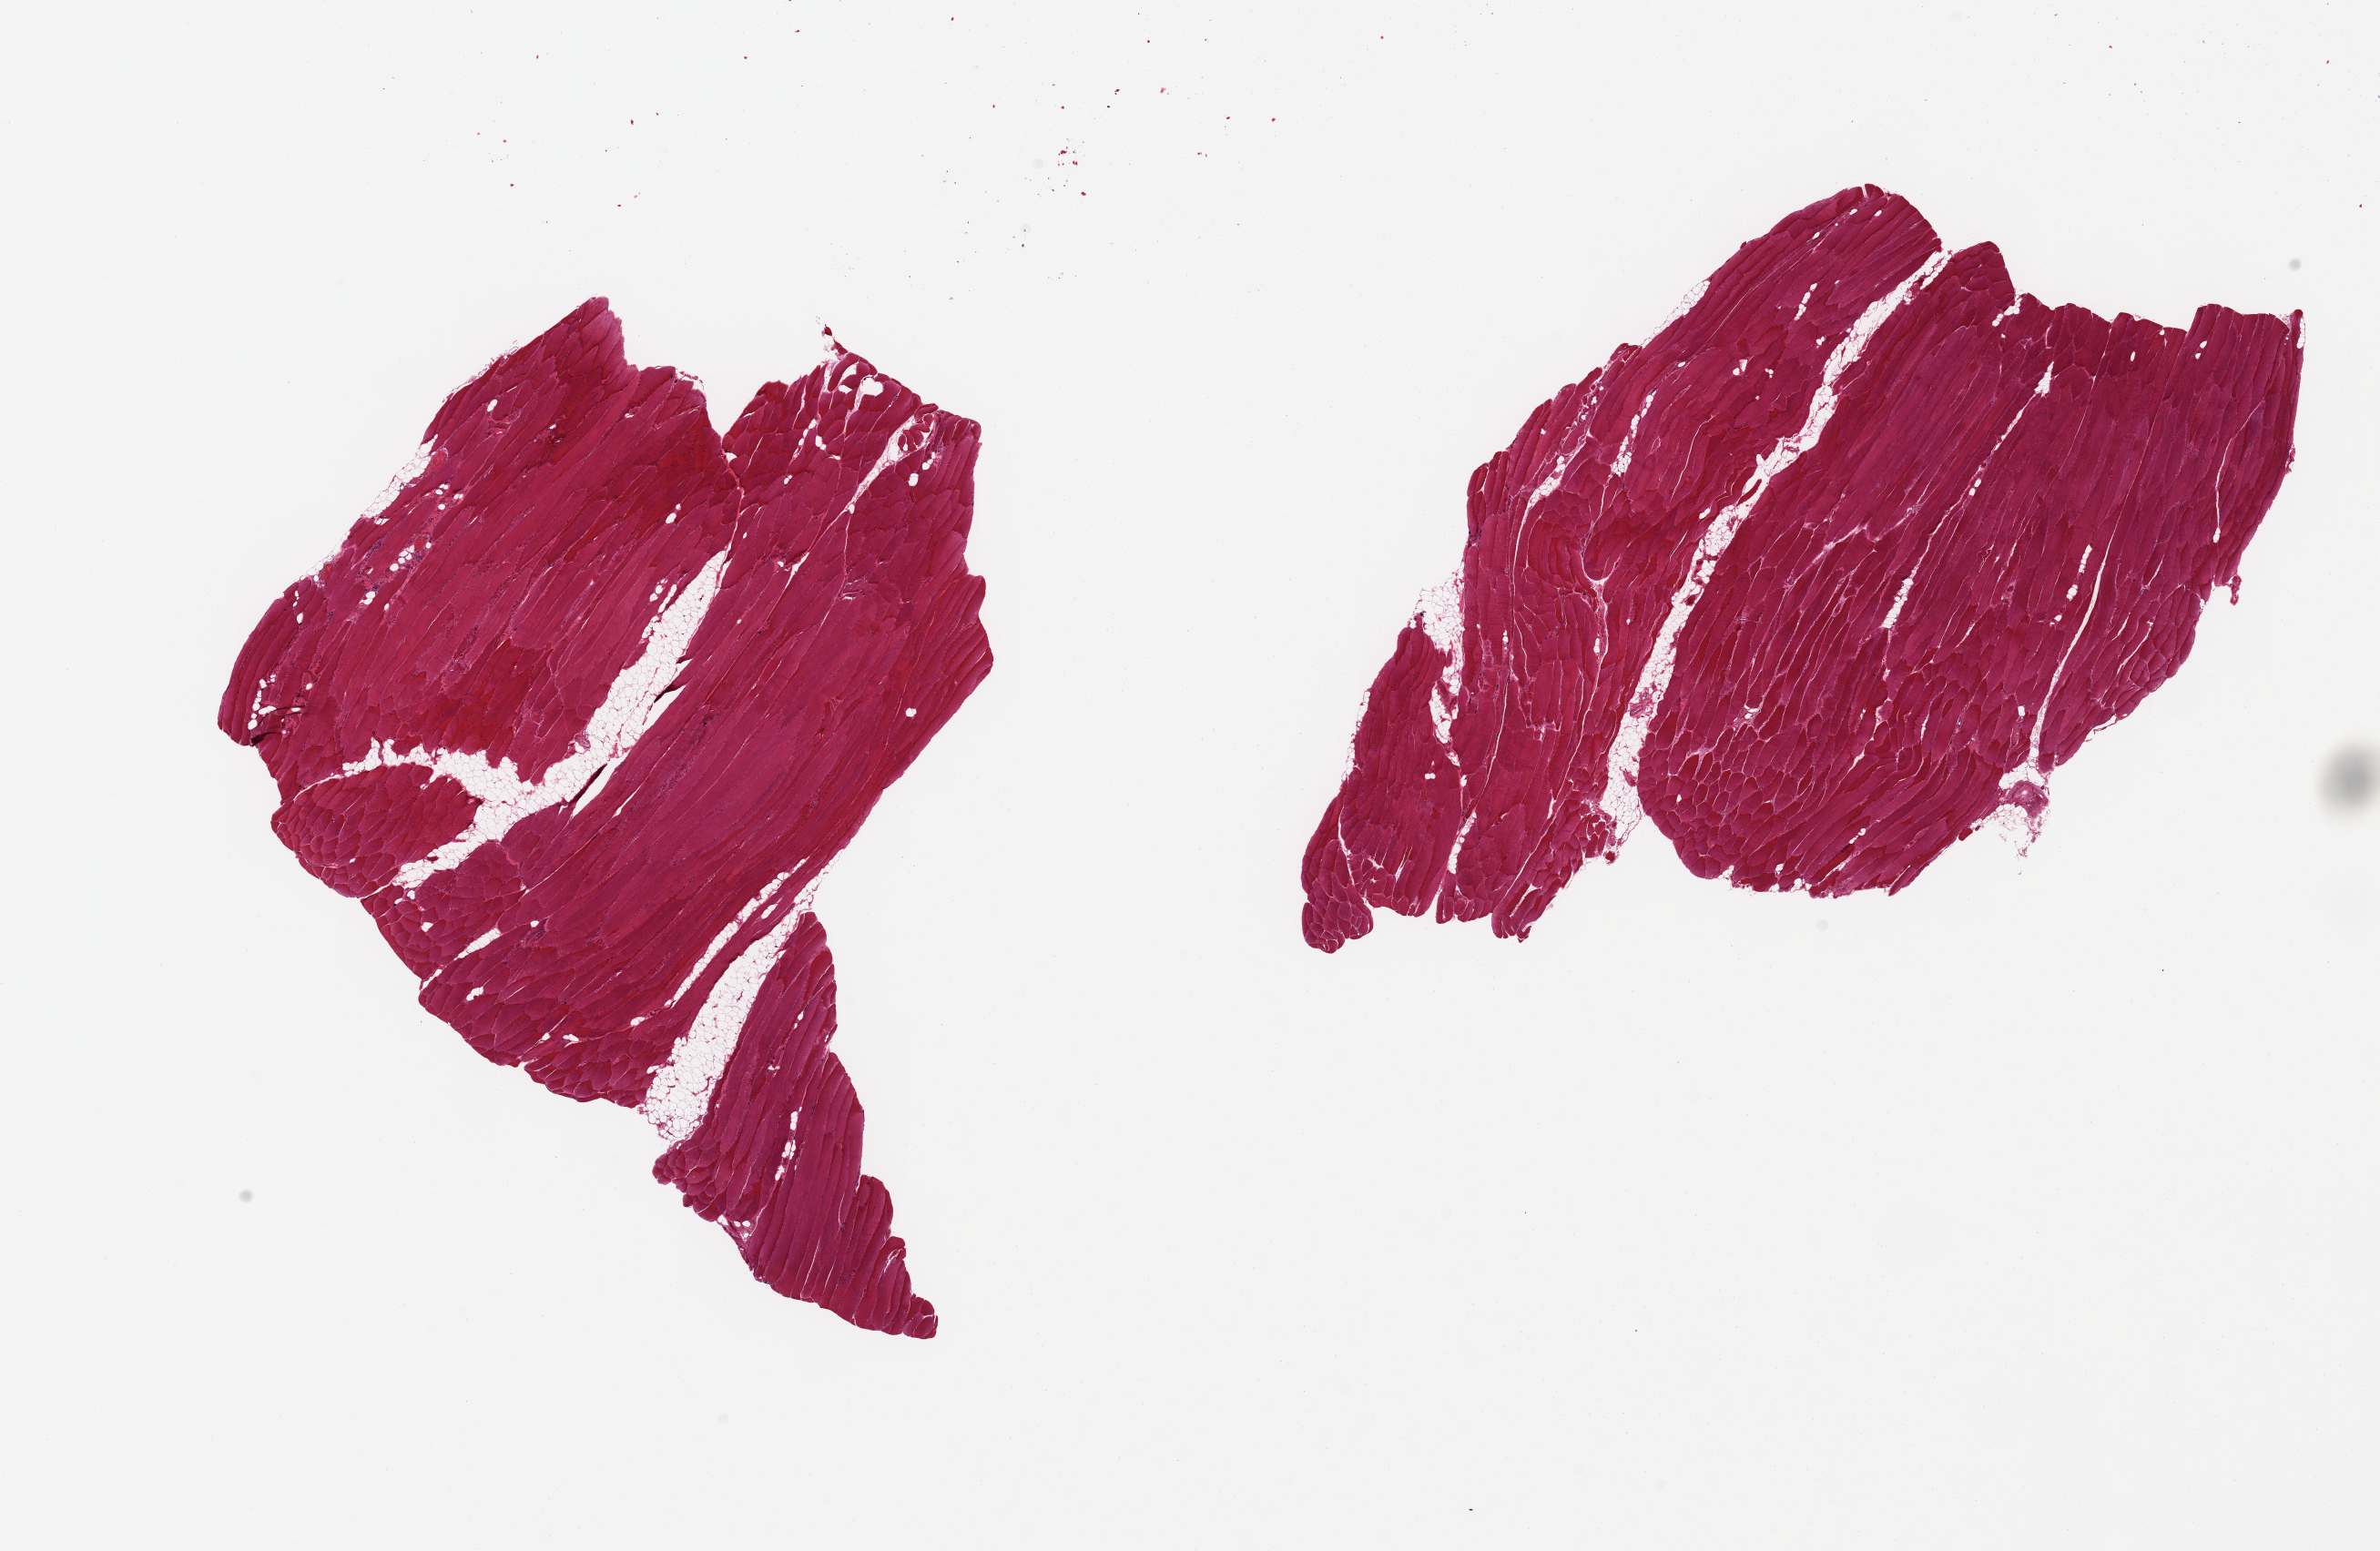
Whole-slide image, hematoxylin and eosin (H&E) stain, brightfield, whole scanned area (about 20.7 x 13.5 mm) shown as a low-resolution overview. PAXgene-fixed paraffin-embedded (PFPE) section. Section of skeletal muscle (target tissue). Donor tissue sample. Donor sex: male.
Pathologist's review note for this sample: 2 pieces; 10 % internal fat.